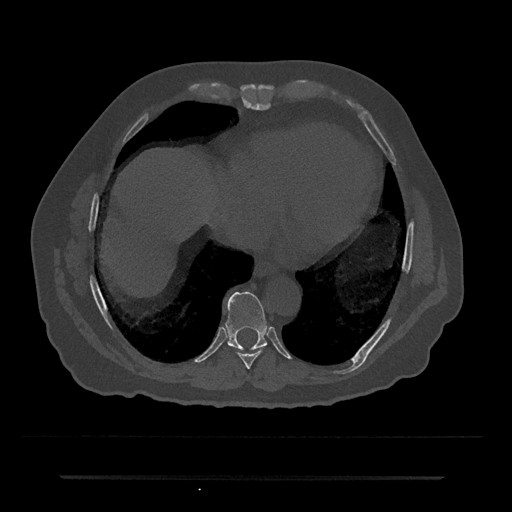
CT including the spine, one axial slice. Slice 303 of 797 in the series (ordered by position). 120 kVp. Bone window (W 1800 / L 400 HU). 512 × 512 image matrix. Patient: male, 69 years. Case-level facts recorded for this patient, not image findings: primary cancer: prostate.
Structures marked on this image (semi-automatic segmentation, software-assisted and operator-edited):
- T8 vertebra: box from (x=237, y=346) to (x=266, y=369) px
- T9 vertebra: (x=225, y=291)–(x=267, y=350)